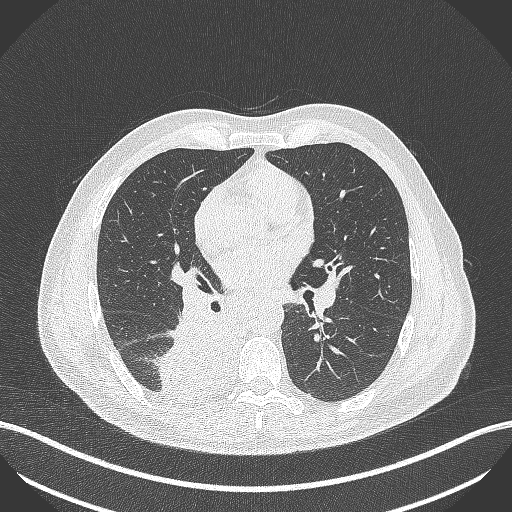
Chest CT, one axial slice. Position 246 of 451 along the scan axis. Reconstruction kernel B70f. 100 kVp. Lung window (W 1500 / L -600 HU). 1 mm slice thickness. 512 × 512 image matrix, field of view 400 × 400 mm. Male patient, age 61 years. From the clinical record (not read from this slice): clinical TNM (as recorded): T1 N0 M0; histopathological grade: G3.
Outlined on this slice (rectangle marked by the reading radiologist):
- lung tumour (recorded histology: small cell carcinoma): bounding box (x1, y1, x2, y2) in pixels: (156, 302, 246, 401)